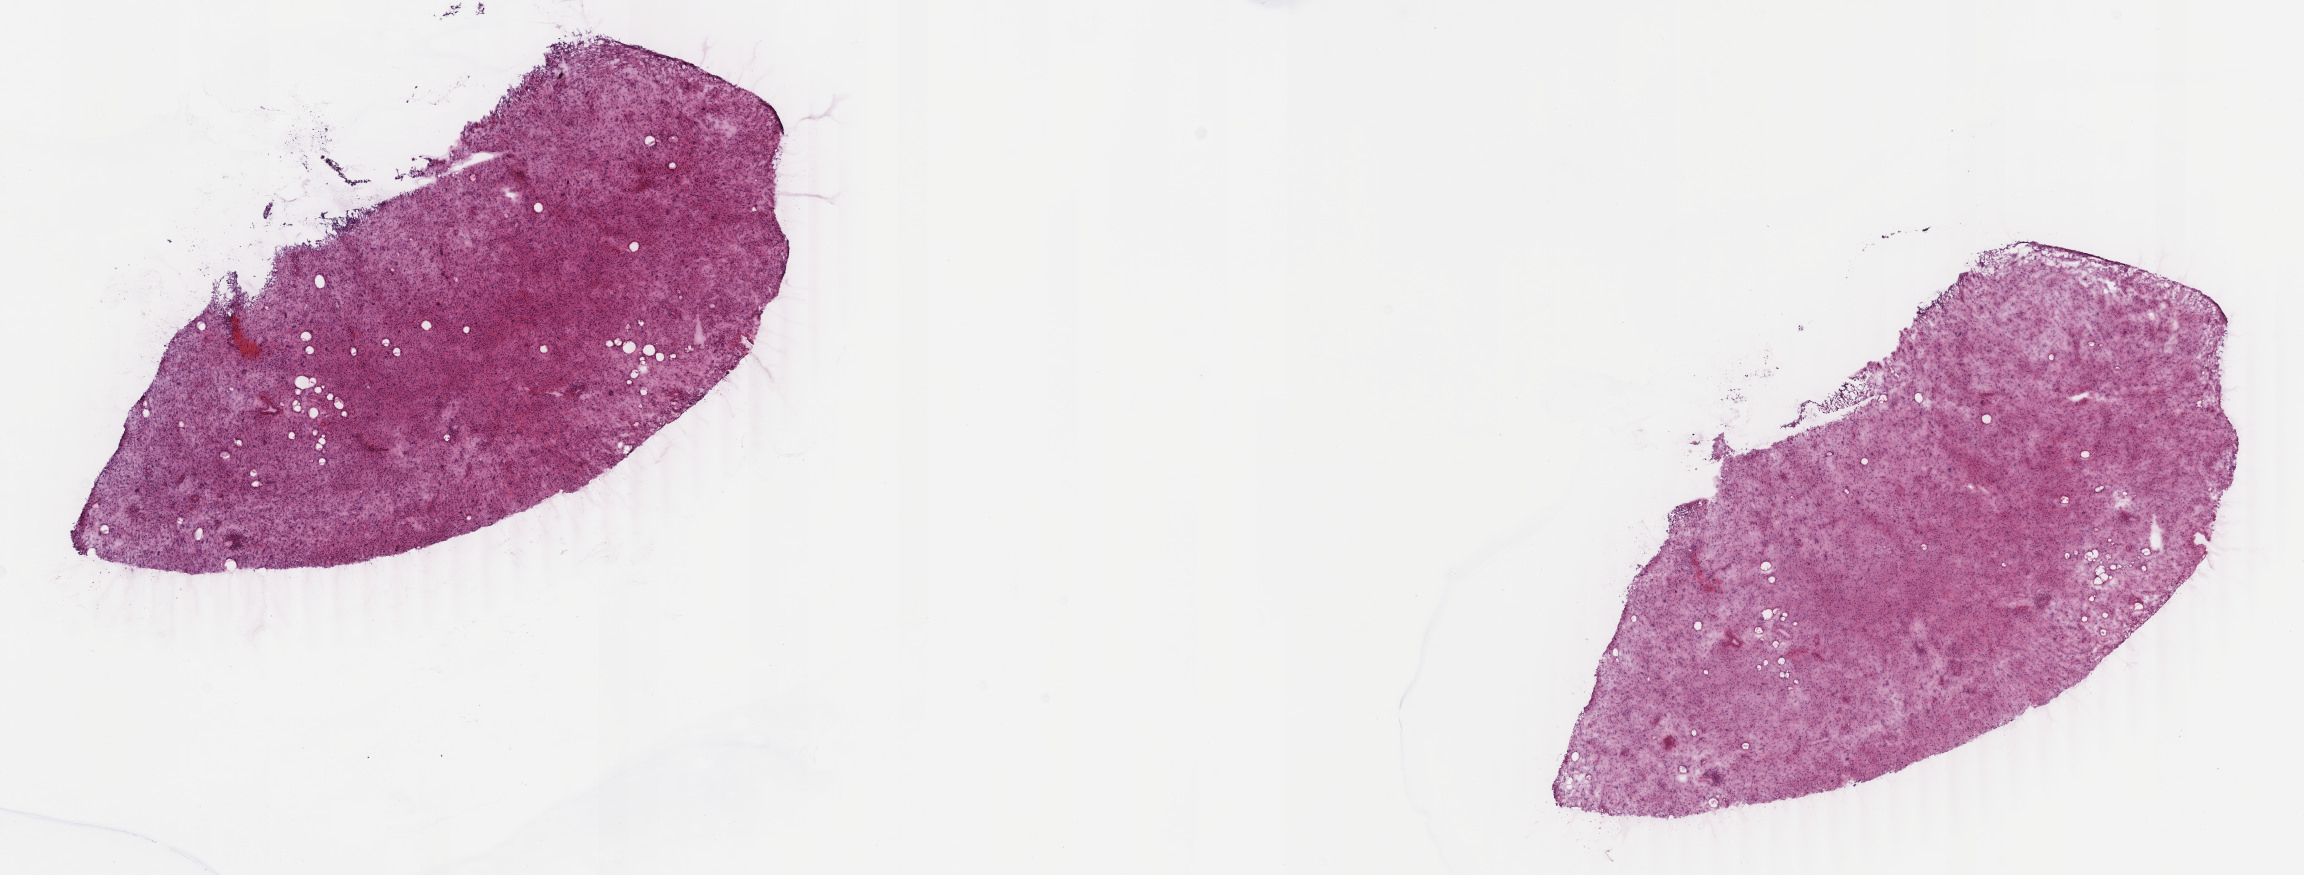
Digitized Hematoxylin and eosin (H&E) stained tissue section (whole slide), low-resolution overview of the scanned area, about 18.3 x 7.0 mm (acquisition: 40x scan); frozen section from the top of the tissue portion; sample: primary tumour, retroperitoneum and peritoneum. Female patient; age at initial diagnosis 57 years. Composition of this section per pathologist review: tumour cells 75%, tumour nuclei 99%, normal cells 0%, stromal cells 25%, necrosis 0%. Inflammatory infiltration, as recorded: lymphocyte infiltration 1%, monocyte infiltration 0%, neutrophil infiltration 0%.
- histologic diagnosis: Dedifferentiated liposarcoma (retroperitoneum)